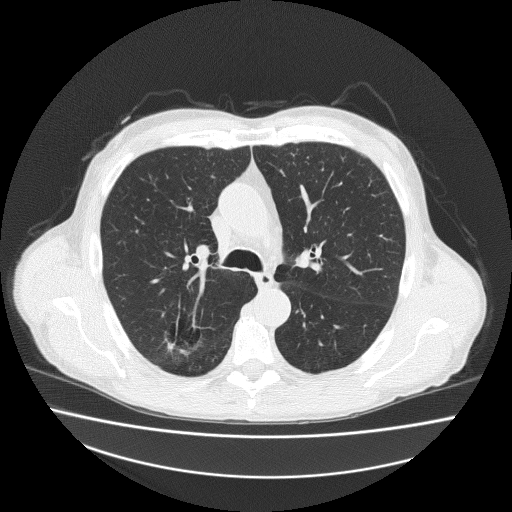
Low-dose screening chest CT, axial slice. Second annual screen. Lung window (W 1500 / L -600 HU). Lung (sharp) reconstruction kernel (FC51). Slice 71 of 186 in the series. 512 × 512 image matrix. Male, age 73 years at enrolment. Current smoker at enrolment.
Expert-annotated lung lesion, bounding box <158,313,212,356> (left, top, right, bottom; pixels). Screening reader's record for this exam: no non-calcified nodule ≥4 mm recorded. Official screen result: negative screen, minor abnormalities not suspicious for lung cancer. Lung cancer was diagnosed 418 days after this screen: adenosquamous carcinoma, right upper lobe, well differentiated (G1), stage IA (AJCC 6th edition), 20 mm at pathology.